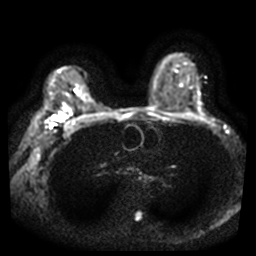
Breast MRI, one axial slice; slice 28 of 44 in the series (ordered by position); diffusion-weighted series; image 2 of 4 stored at this slice position (different b-values; order by instance number); 3 T; 256 × 256 image matrix. Female patient.
Outlined on this slice (expert manual segmentation):
- tumour on diffusion-weighted imaging: bounding box <54,115,65,120> (left, top, right, bottom; pixels)